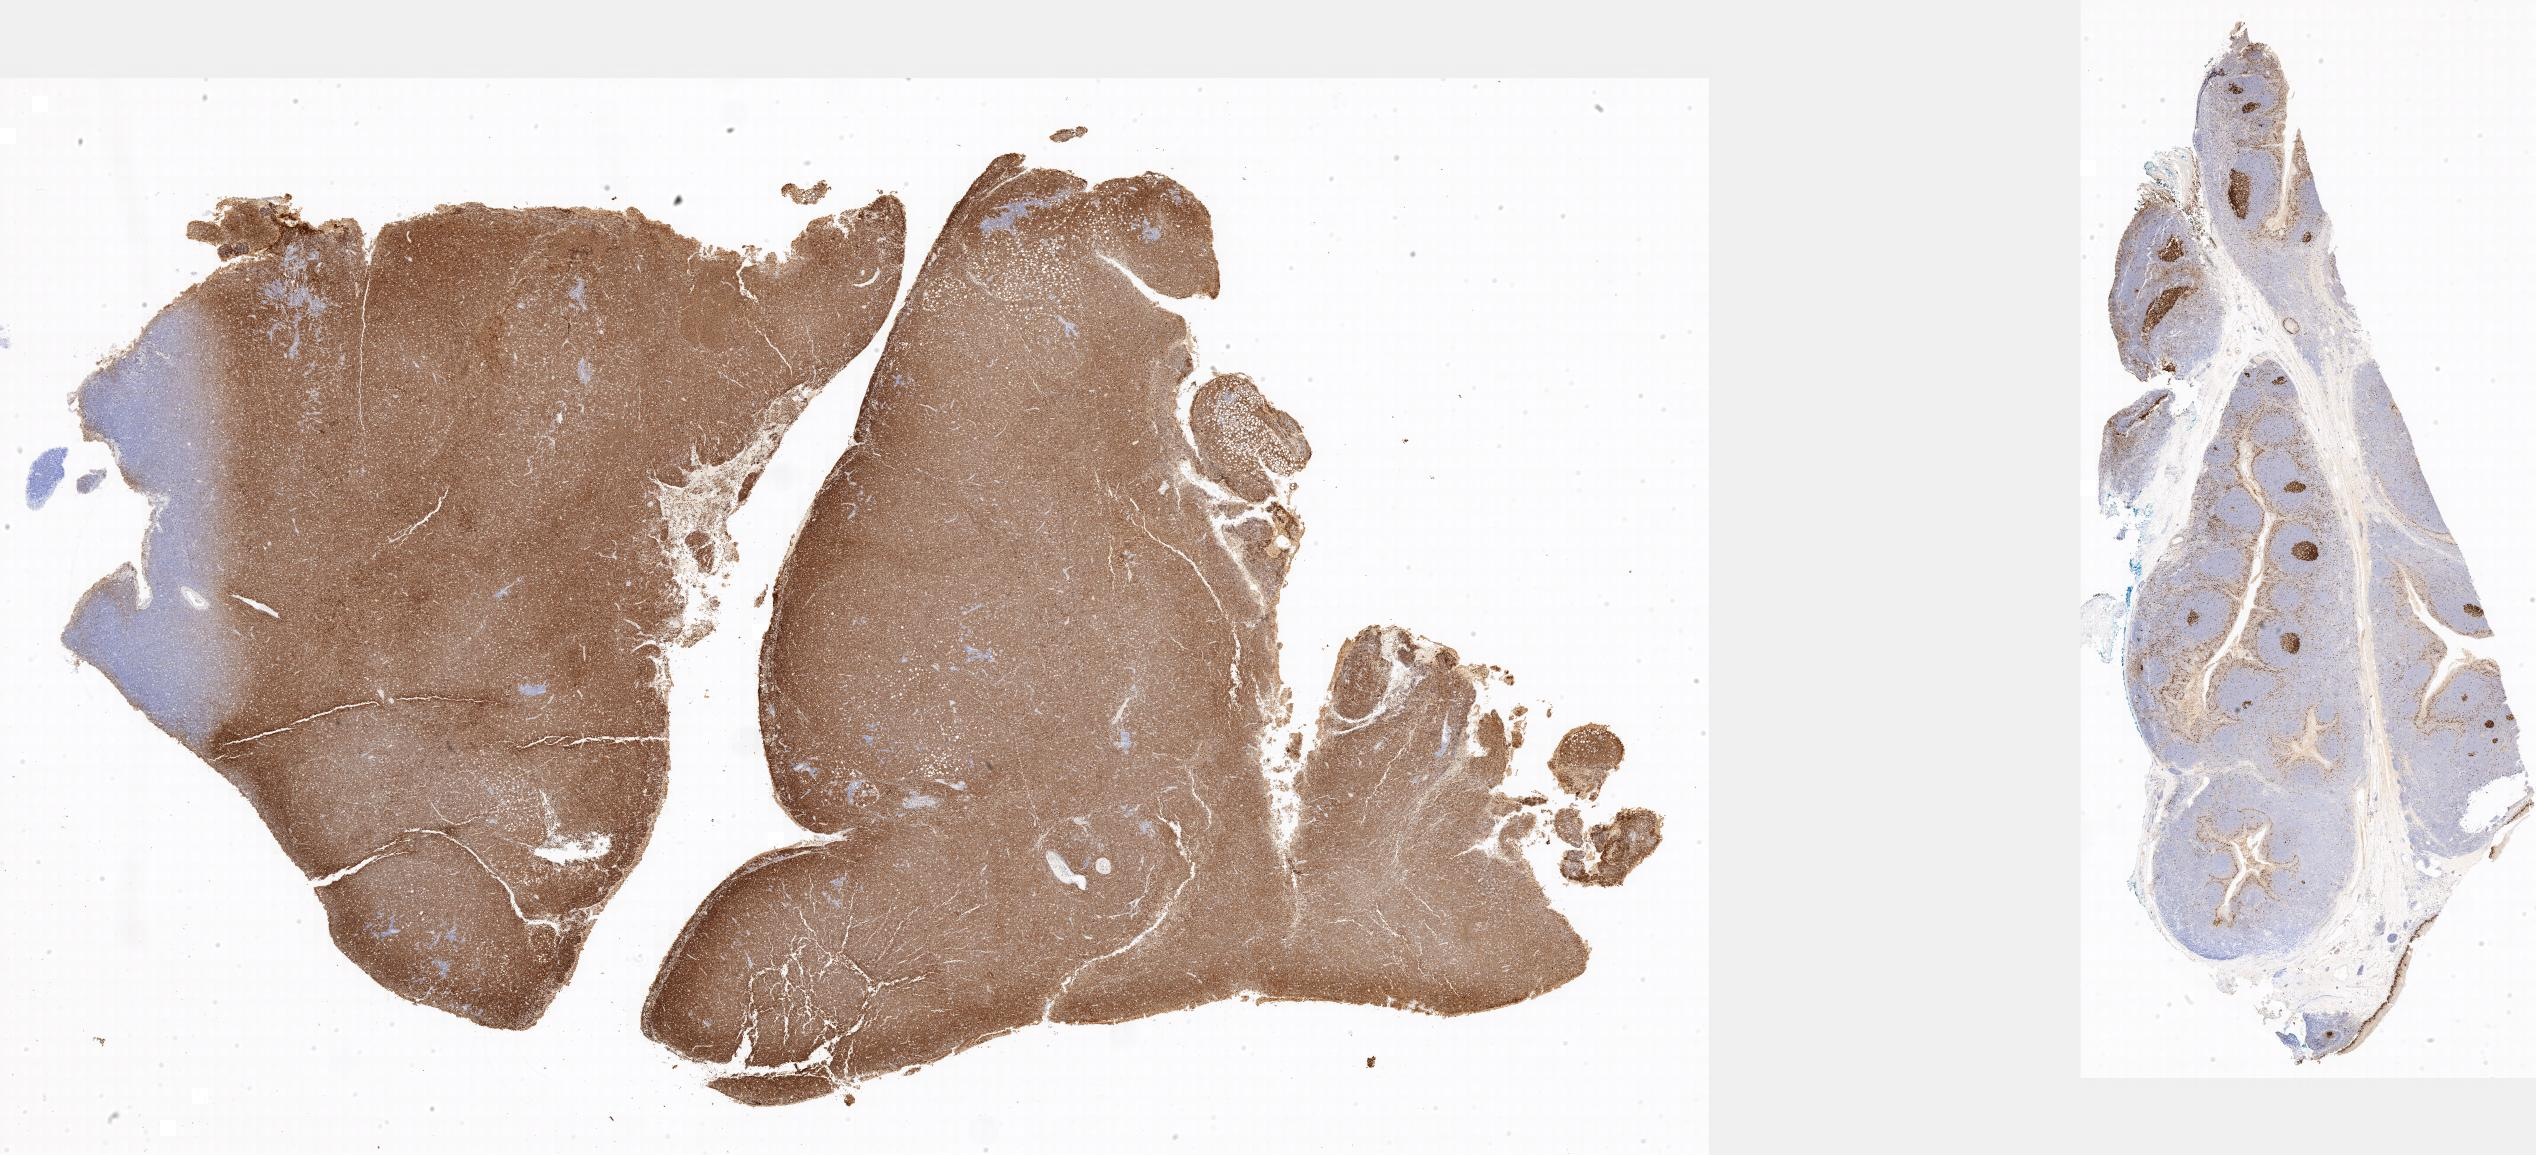
Immunohistochemistry (IHC) whole-slide image stained for Ki-67 — whole scanned area shown as a low-resolution overview. Specimen: tumor tissue. Site: peritoneum. Patient: male, age at initial diagnosis 9 years.
* histologic diagnosis: Burkitt lymphoma, NOS